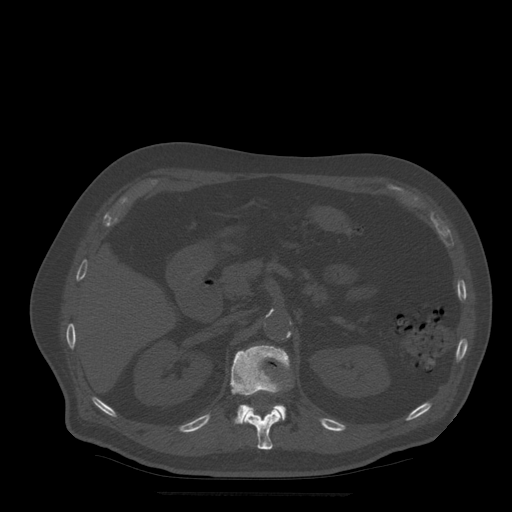
CT including the spine, one axial slice; slice 208 of 522 in the series (ordered by position); bone window (W 1800 / L 400 HU); 1.25 mm slice thickness; 512 × 512 image matrix, field of view 420 × 420 mm. Patient age 72 years. Case-level facts recorded for this patient, not image findings: primary cancer: prostate.
Outlined on this slice (semi-automatic segmentation, software-assisted and operator-edited):
- L1 vertebra: bounding box [x1, y1, x2, y2] px = [230, 345, 290, 424]
- T12 vertebra: [243, 408, 283, 450]